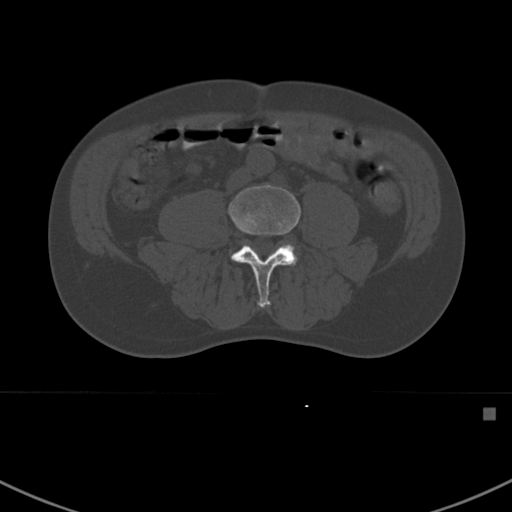
CT including the spine, one axial slice. Slice 237 of 412 in the series (ordered by position). Reconstruction kernel Br40s. 120 kVp. Bone window (W 1800 / L 400 HU). 1.5 mm slice thickness. 512 × 512 image matrix, field of view 358 × 358 mm. Patient: male, 59 years. From the clinical record (not read from this slice): primary cancer: prostate.
Outlined on this slice (semi-automatically segmented with operator editing):
- L4 vertebra: bounding box <227,184,301,307> (left, top, right, bottom; pixels)
- L5 vertebra: <290,246,296,256>